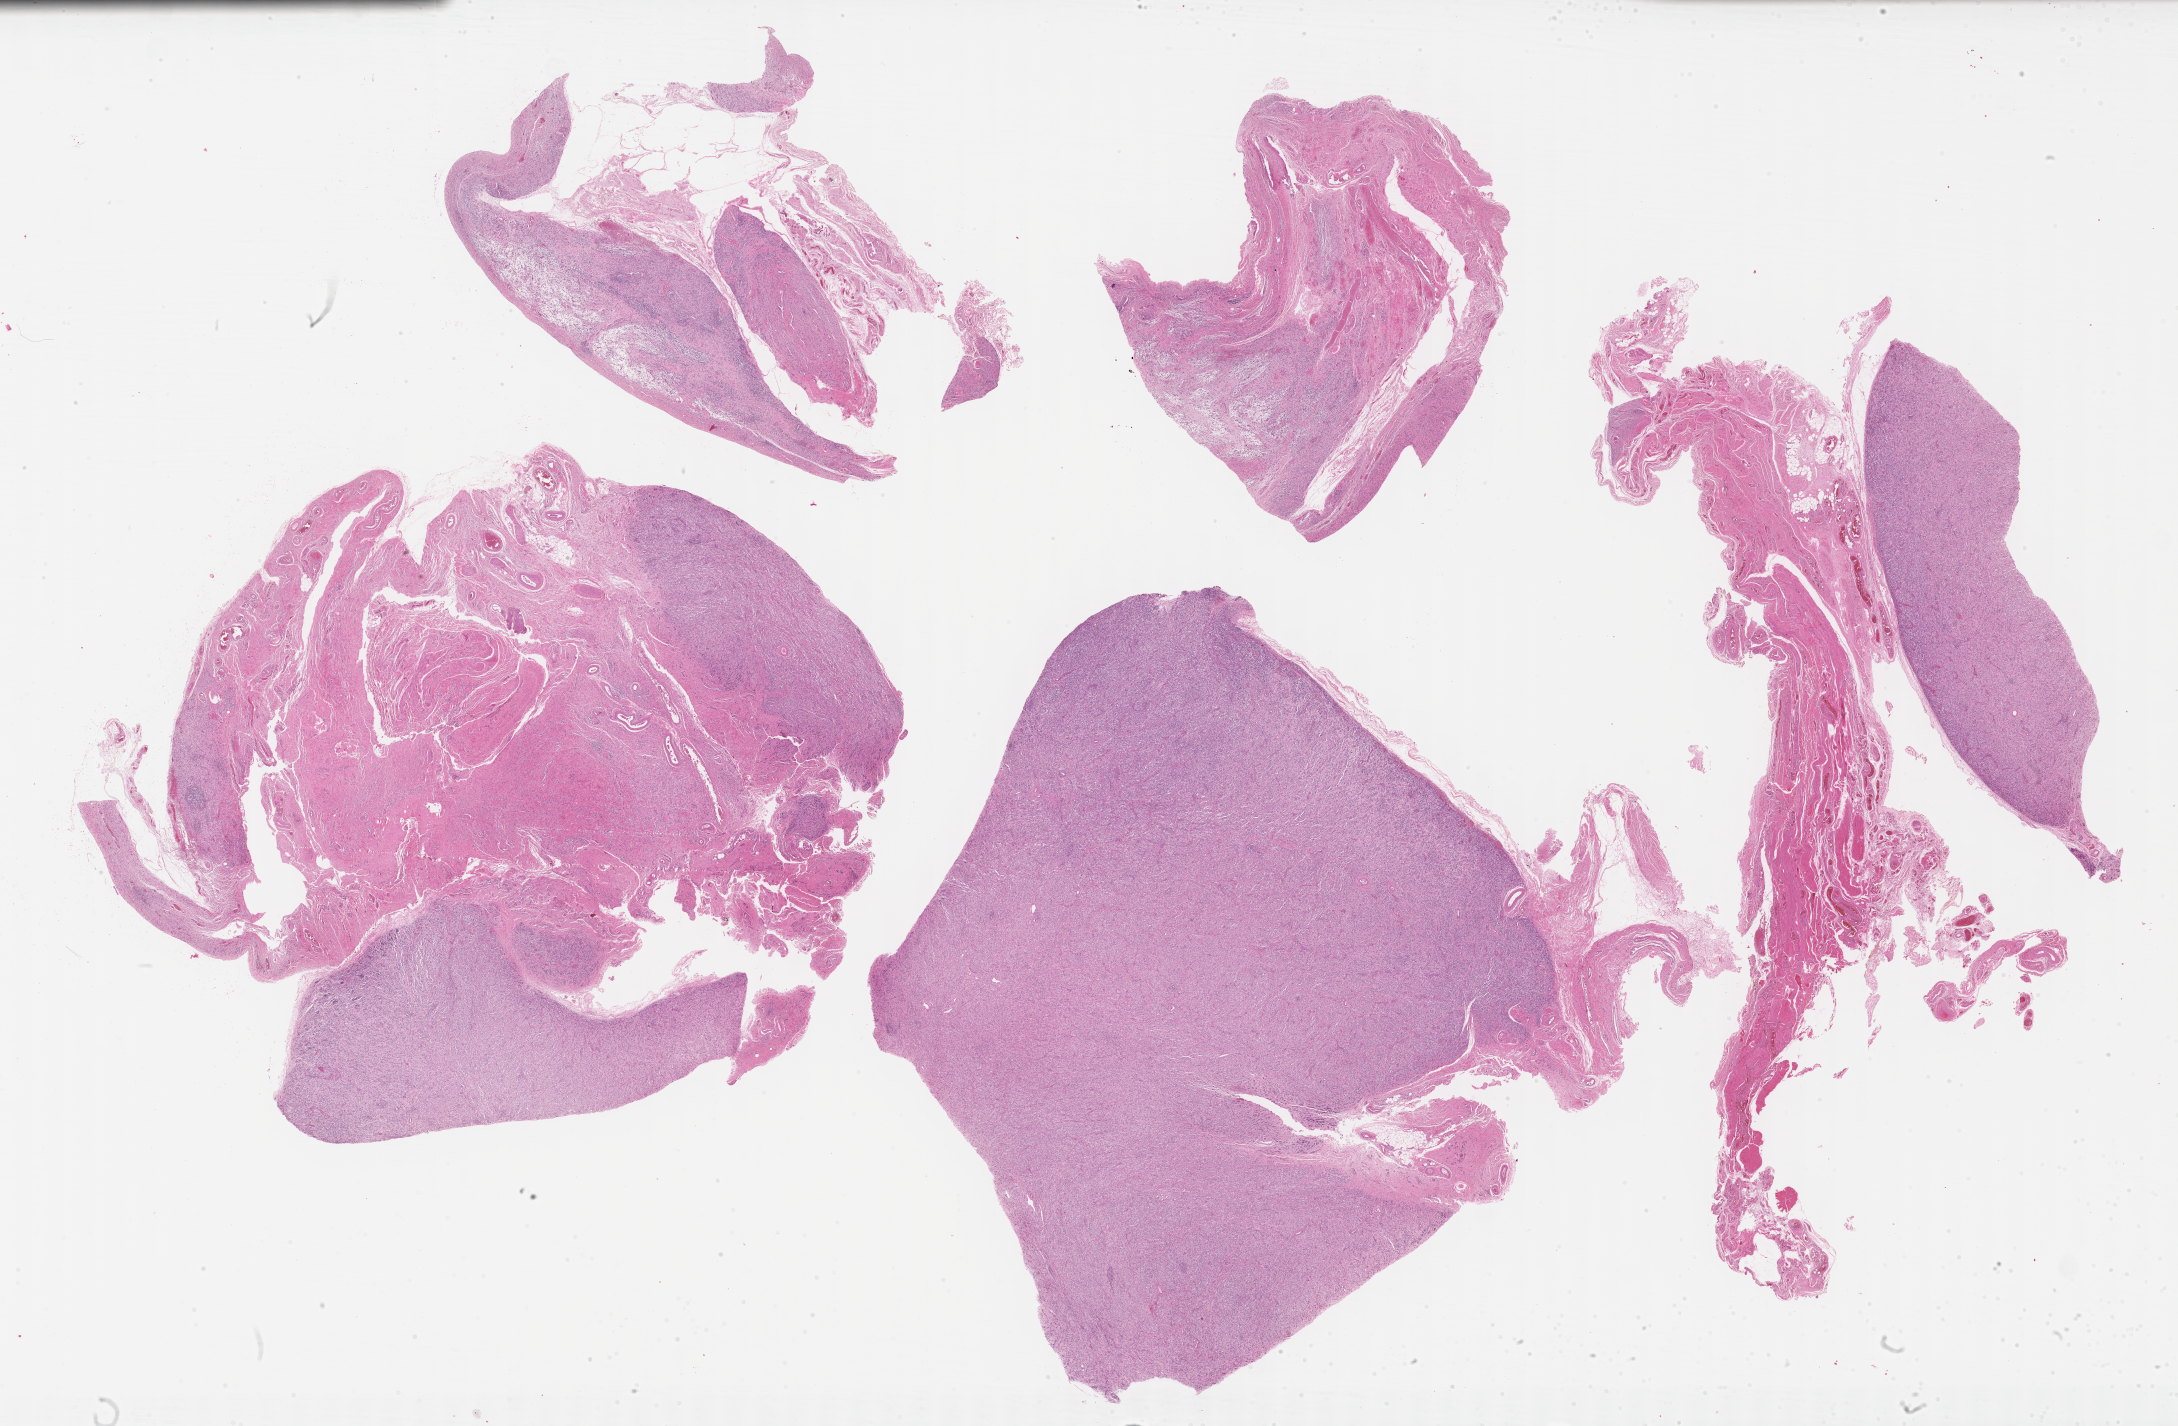
Digitized hematoxylin and eosin (H&E)-stained section of tumor tissue — shown as a low-resolution overview of the whole scanned area (about 35.2 x 23.1 mm), formalin-fixed paraffin-embedded section, site: paratesticular, left. Patient: male, age 2.5 years at diagnosis.
* stage (as recorded): 1
* diagnosis: rhabdomyosarcoma; histological classification: spindle cell rhabdomyosarcoma
* primary site (case record): testis-paratesticular
* metastatic status at presentation (as recorded): non-metastatic (confirmed)